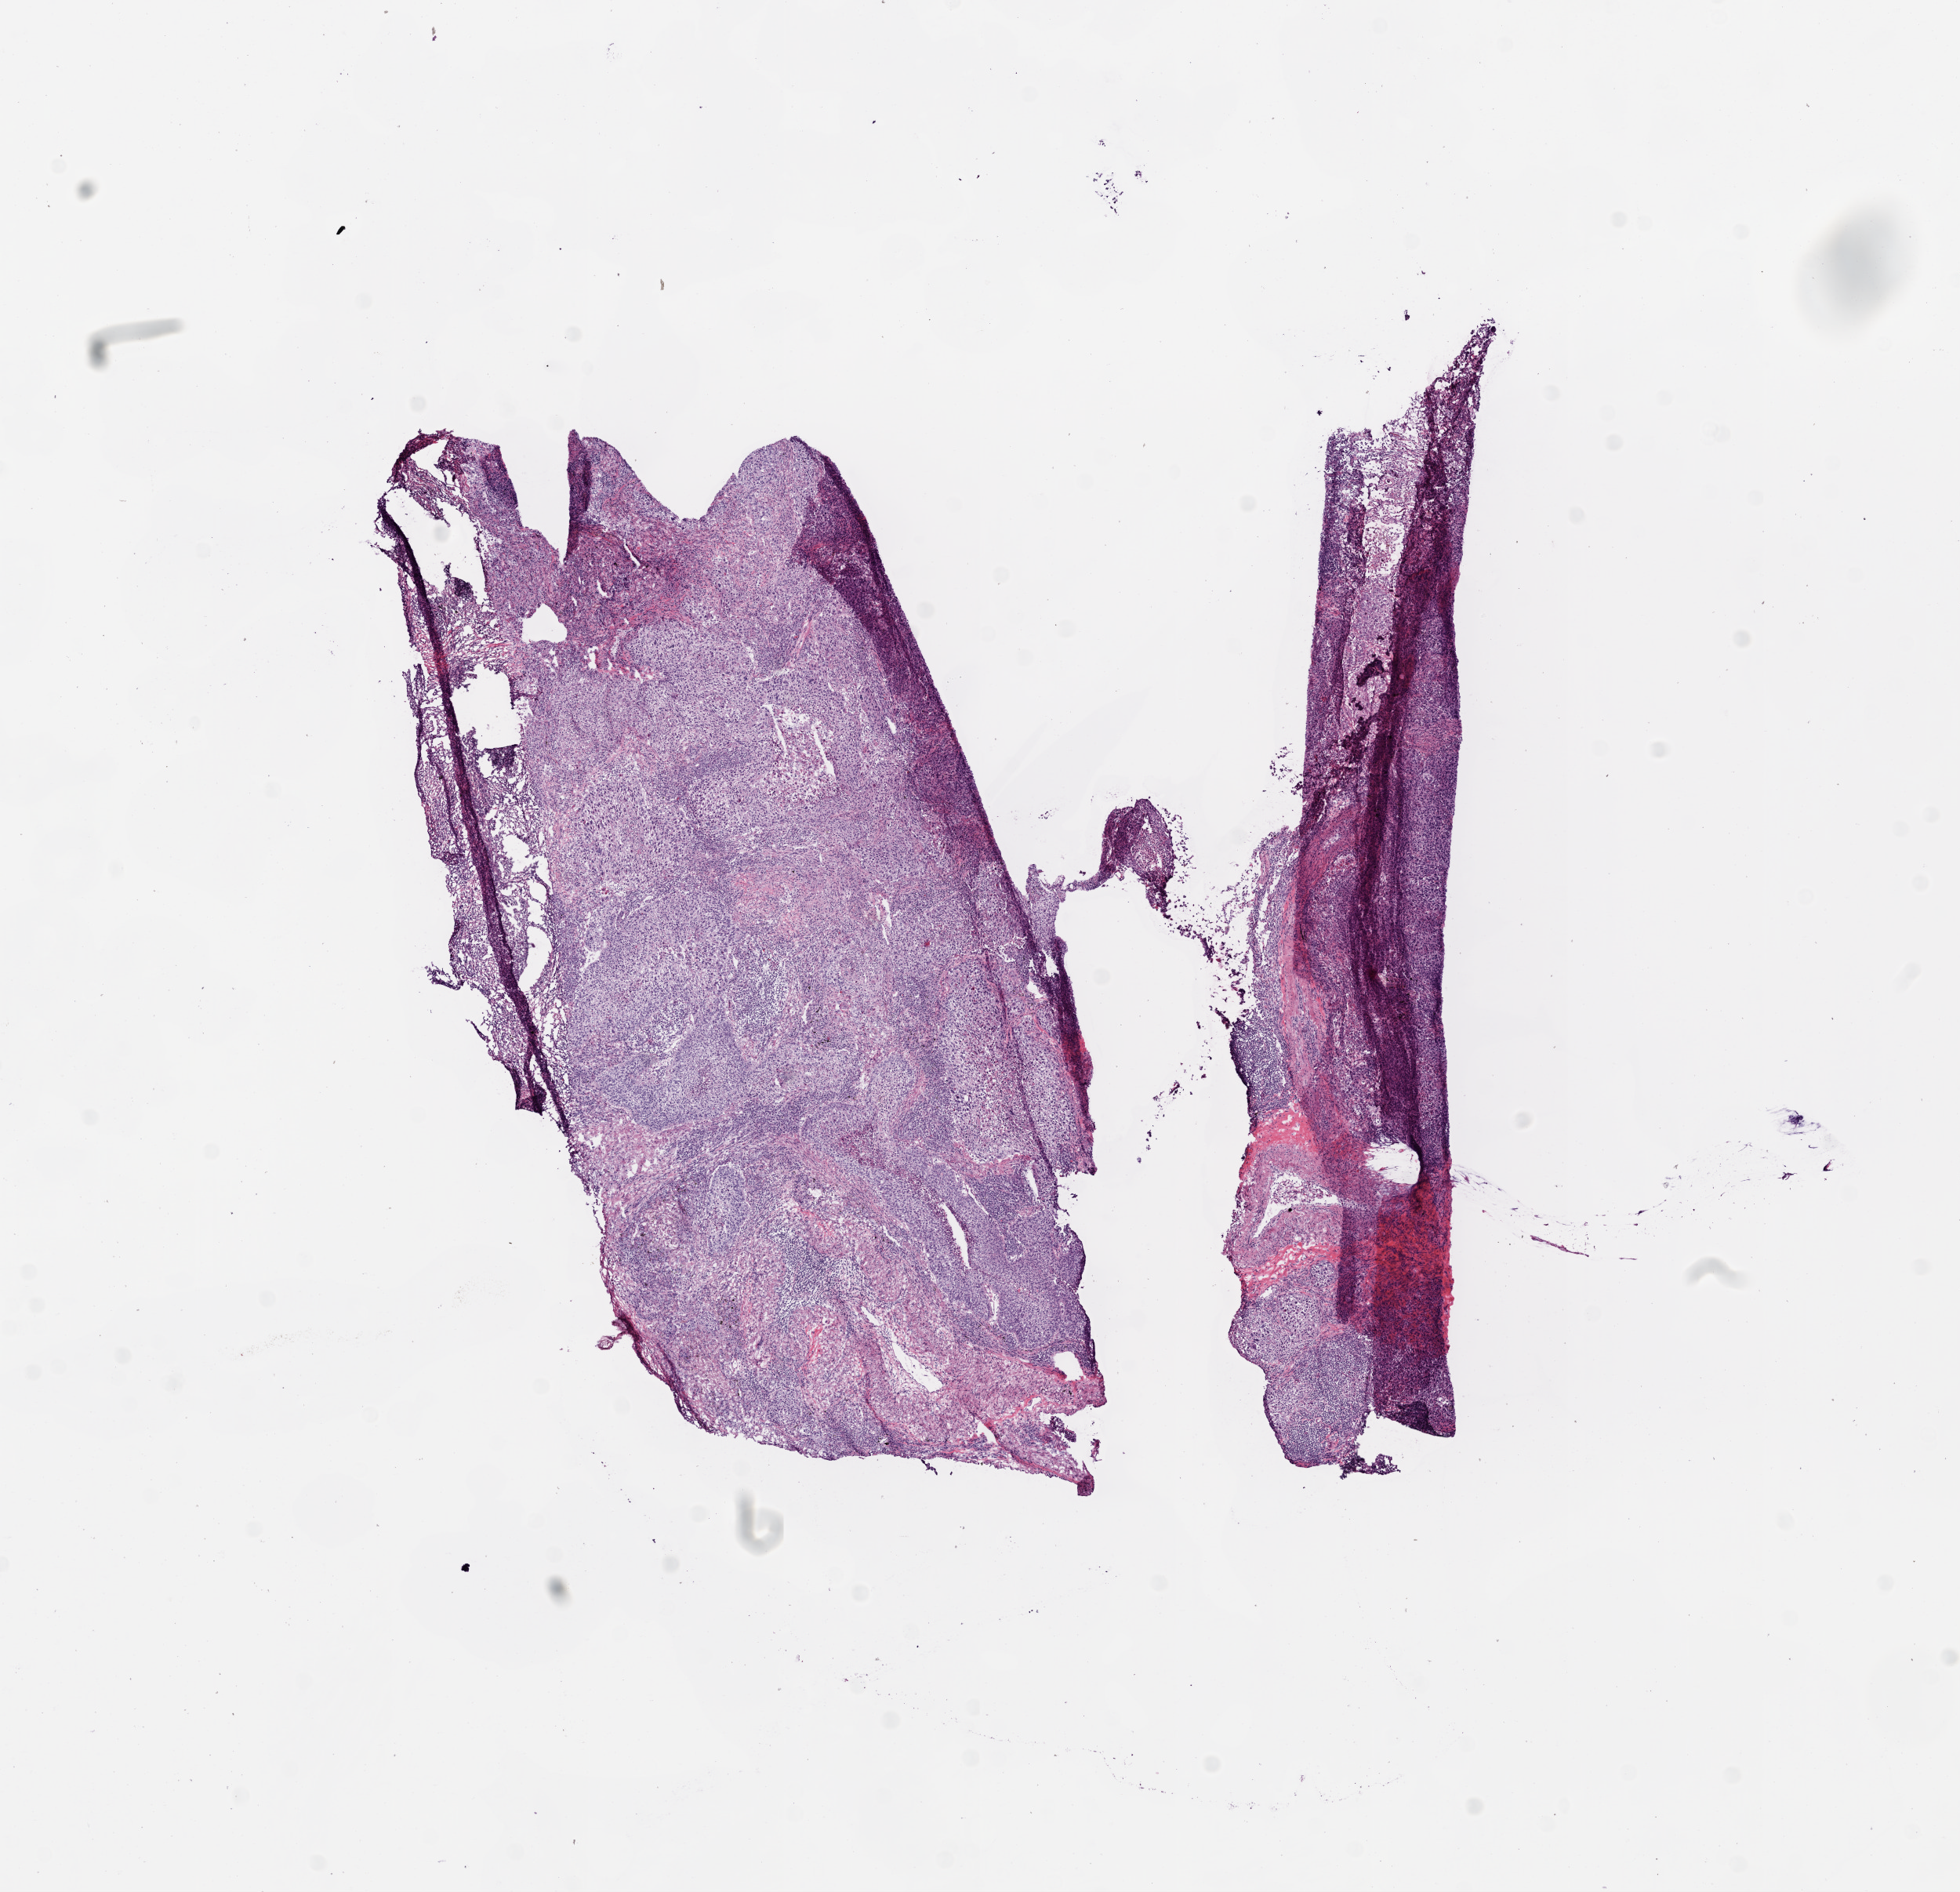
Hematoxylin and eosin (H&E) stained whole-slide image — a low-resolution overview of the entire scanned area, about 10.0 x 9.7 mm. Frozen section from the bottom of the tissue portion. Primary tumour sample from the lung. Male, age 60 years at initial diagnosis.
Pathologic diagnosis: Squamous cell carcinoma, NOS (upper lobe, lung).